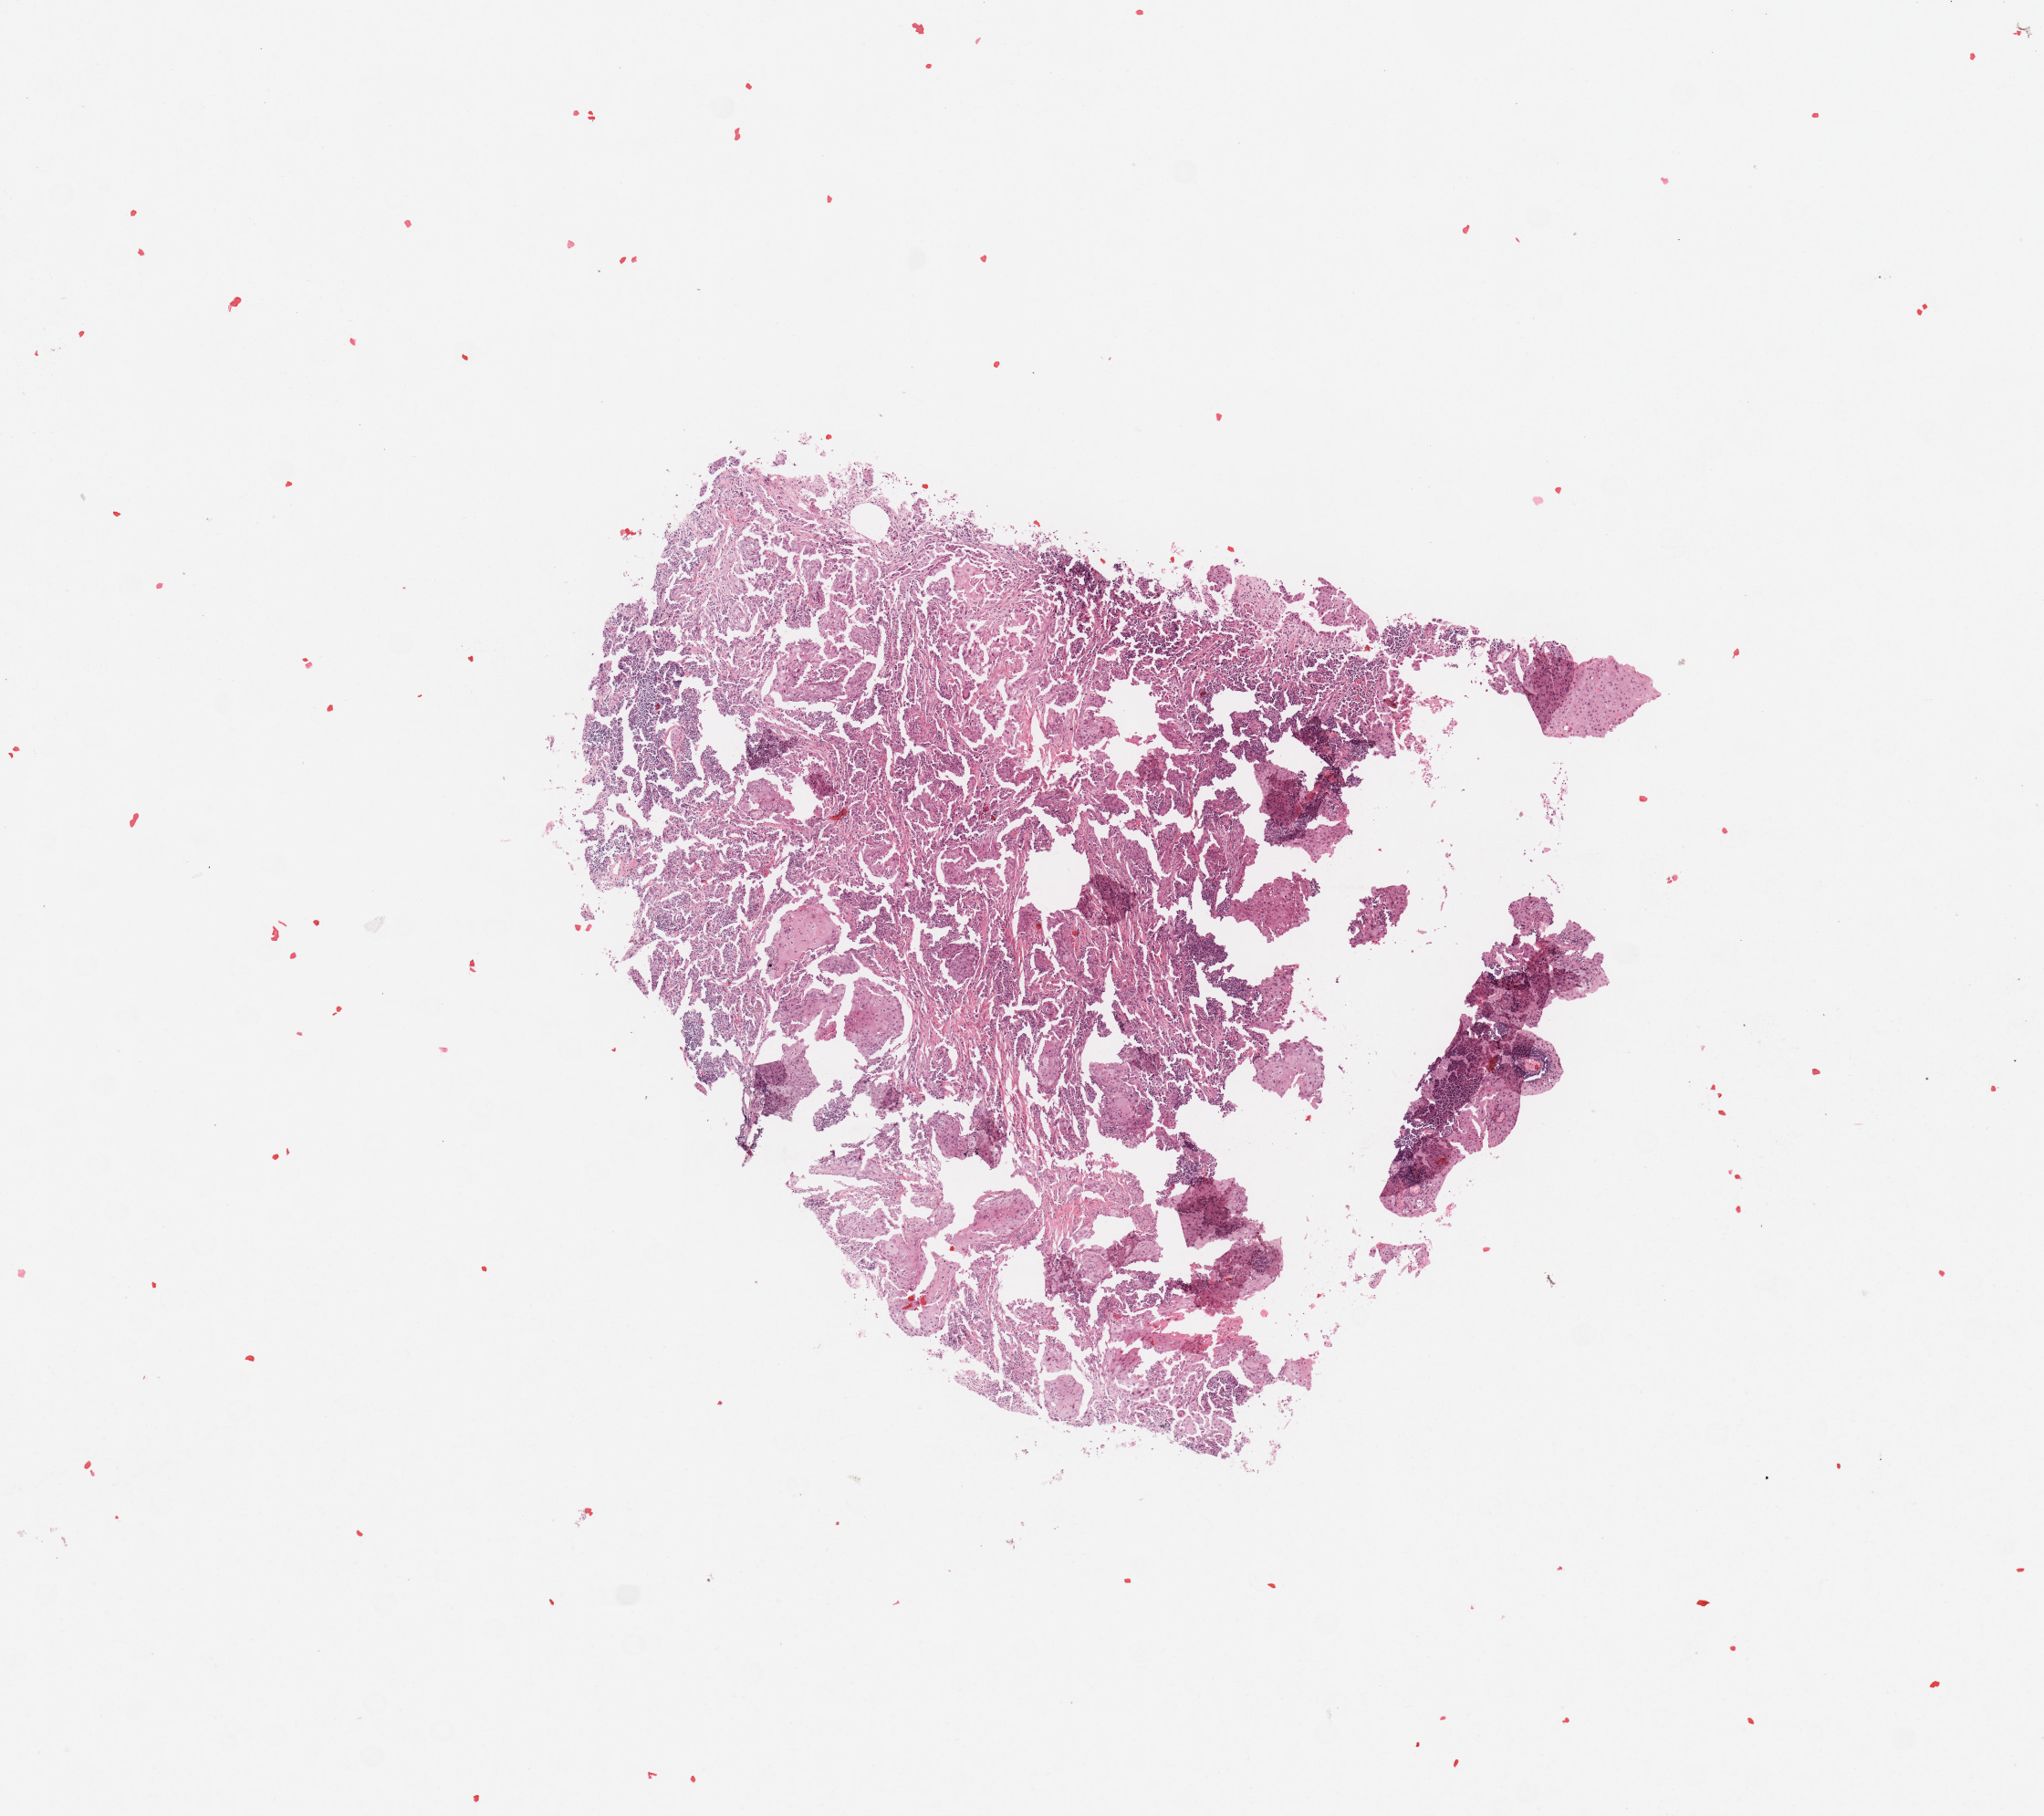
H&E-stained whole-slide image, low-resolution overview of the scanned area, about 8.9 x 7.9 mm (acquisition: 20x scan). Tumour tissue sample, sampled site: lung. Patient: female, age 56 years. Histologic grade: G3 (poorly differentiated). Slide review estimates, as recorded: tumour nuclei 65%, necrosis 5%.
Diagnosis: Squamous cell carcinoma, NOS. Primary tumour site (as recorded): left lower lobe. AJCC pathologic stage: IIIA.